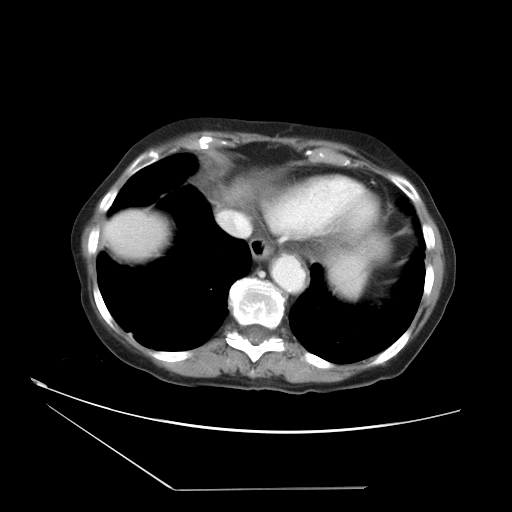
Contrast-enhanced abdominal CT, one axial slice; slice 32 of 36 in the series (ordered by position); 120 kVp; intravenous contrast given; soft-tissue window (W 400 / L 40 HU); 5 mm slice thickness; 512 × 512 image matrix, field of view 384 × 384 mm. Female patient, age 81 years. From the clinical record (not read from this slice): diagnosis: colorectal cancer liver metastases, imaged before liver resection; multiple liver metastases: no; largest metastasis: 1.6 cm.
Annotated regions visible in this slice (expert manual segmentation):
- liver: bounding box [x1, y1, x2, y2] px = [106, 208, 169, 261]
- planned liver remnant (the part of the liver to remain after resection): [105, 208, 170, 261]